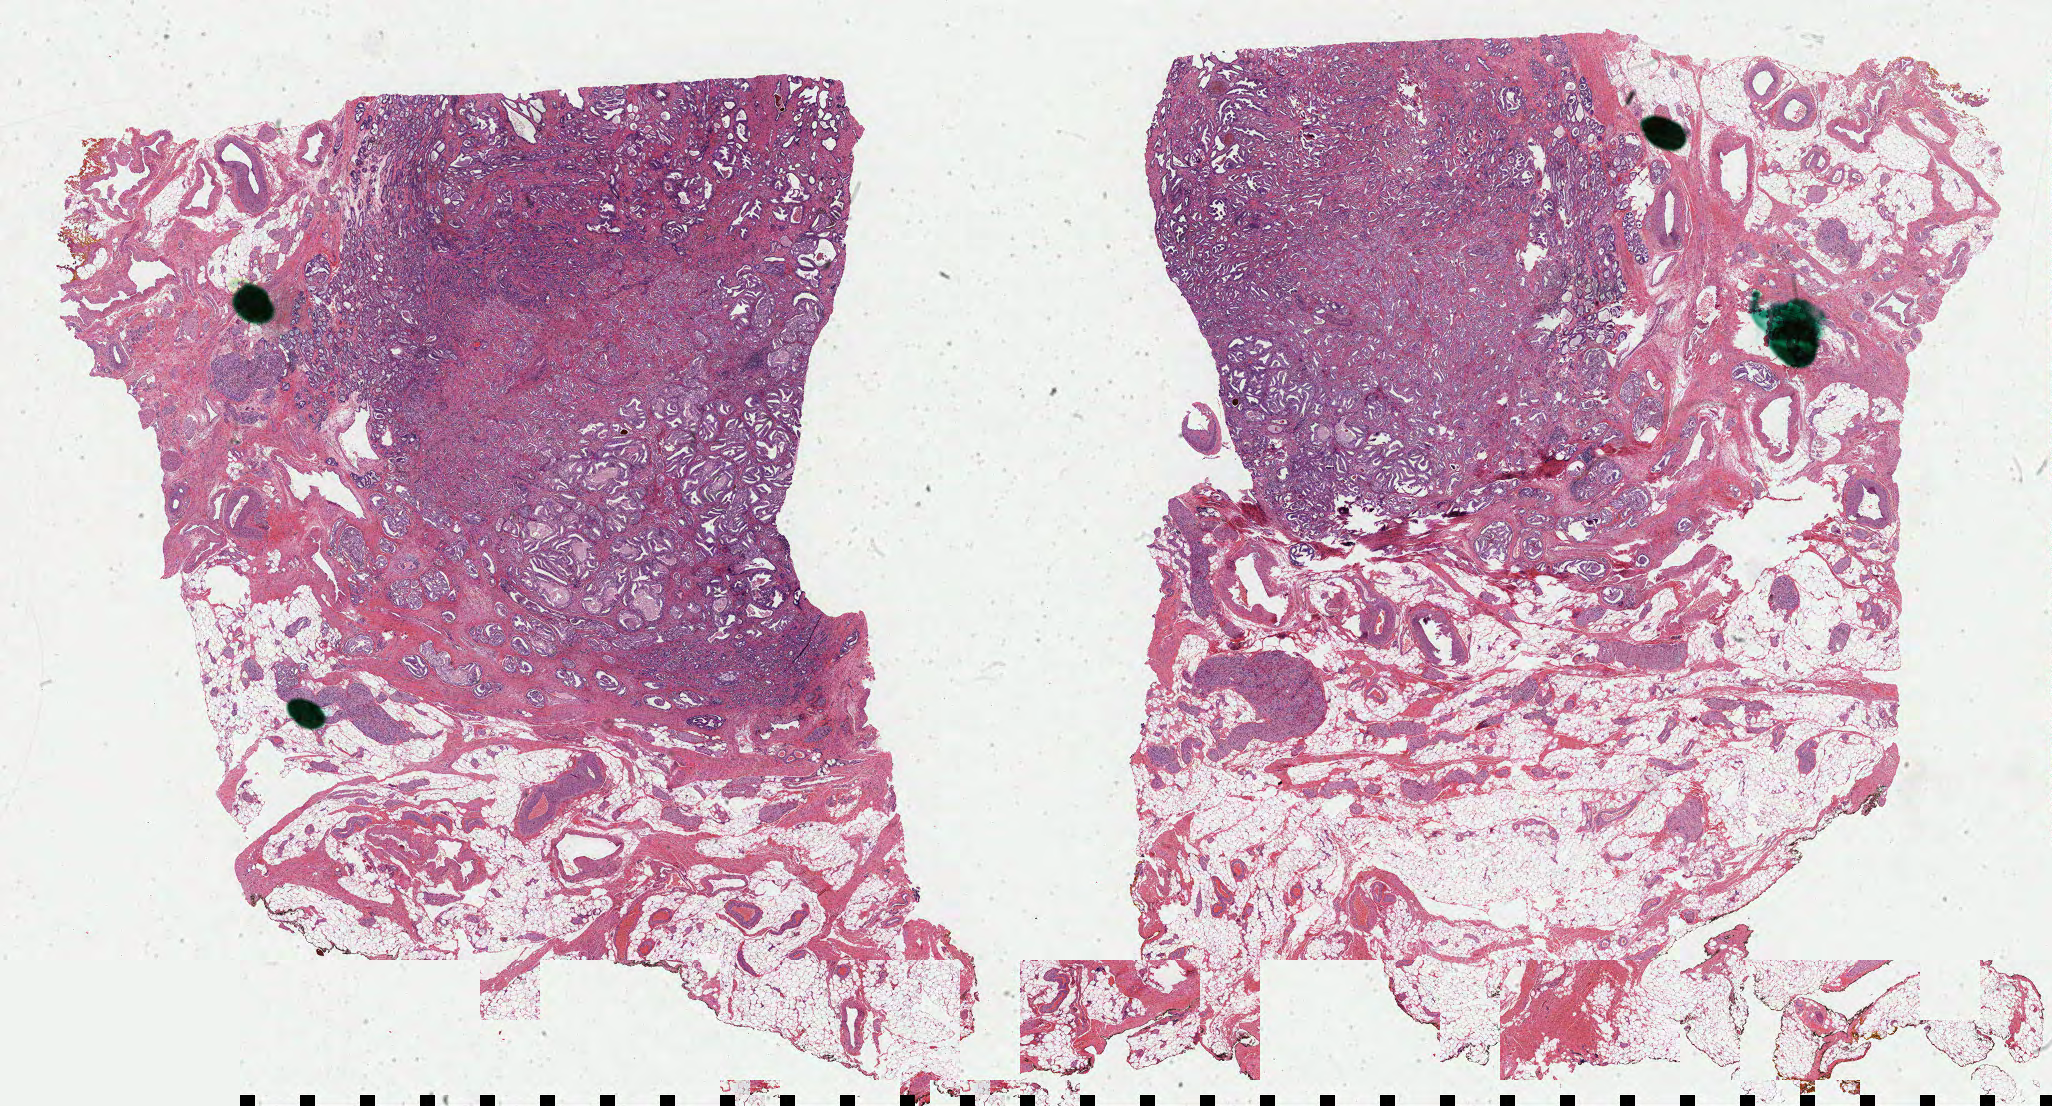
Whole-slide histology image, Hematoxylin and eosin (H&E) stained, shown as a low-resolution overview of the whole scanned area (about 32.6 x 17.6 mm); formalin-fixed paraffin-embedded (FFPE) diagnostic section; primary tumour sample from the prostate. Male, age 50 years at initial diagnosis. Gleason score: 7 (4+3).
Diagnosis: Adenocarcinoma, NOS (prostate gland). Laterality: bilateral.